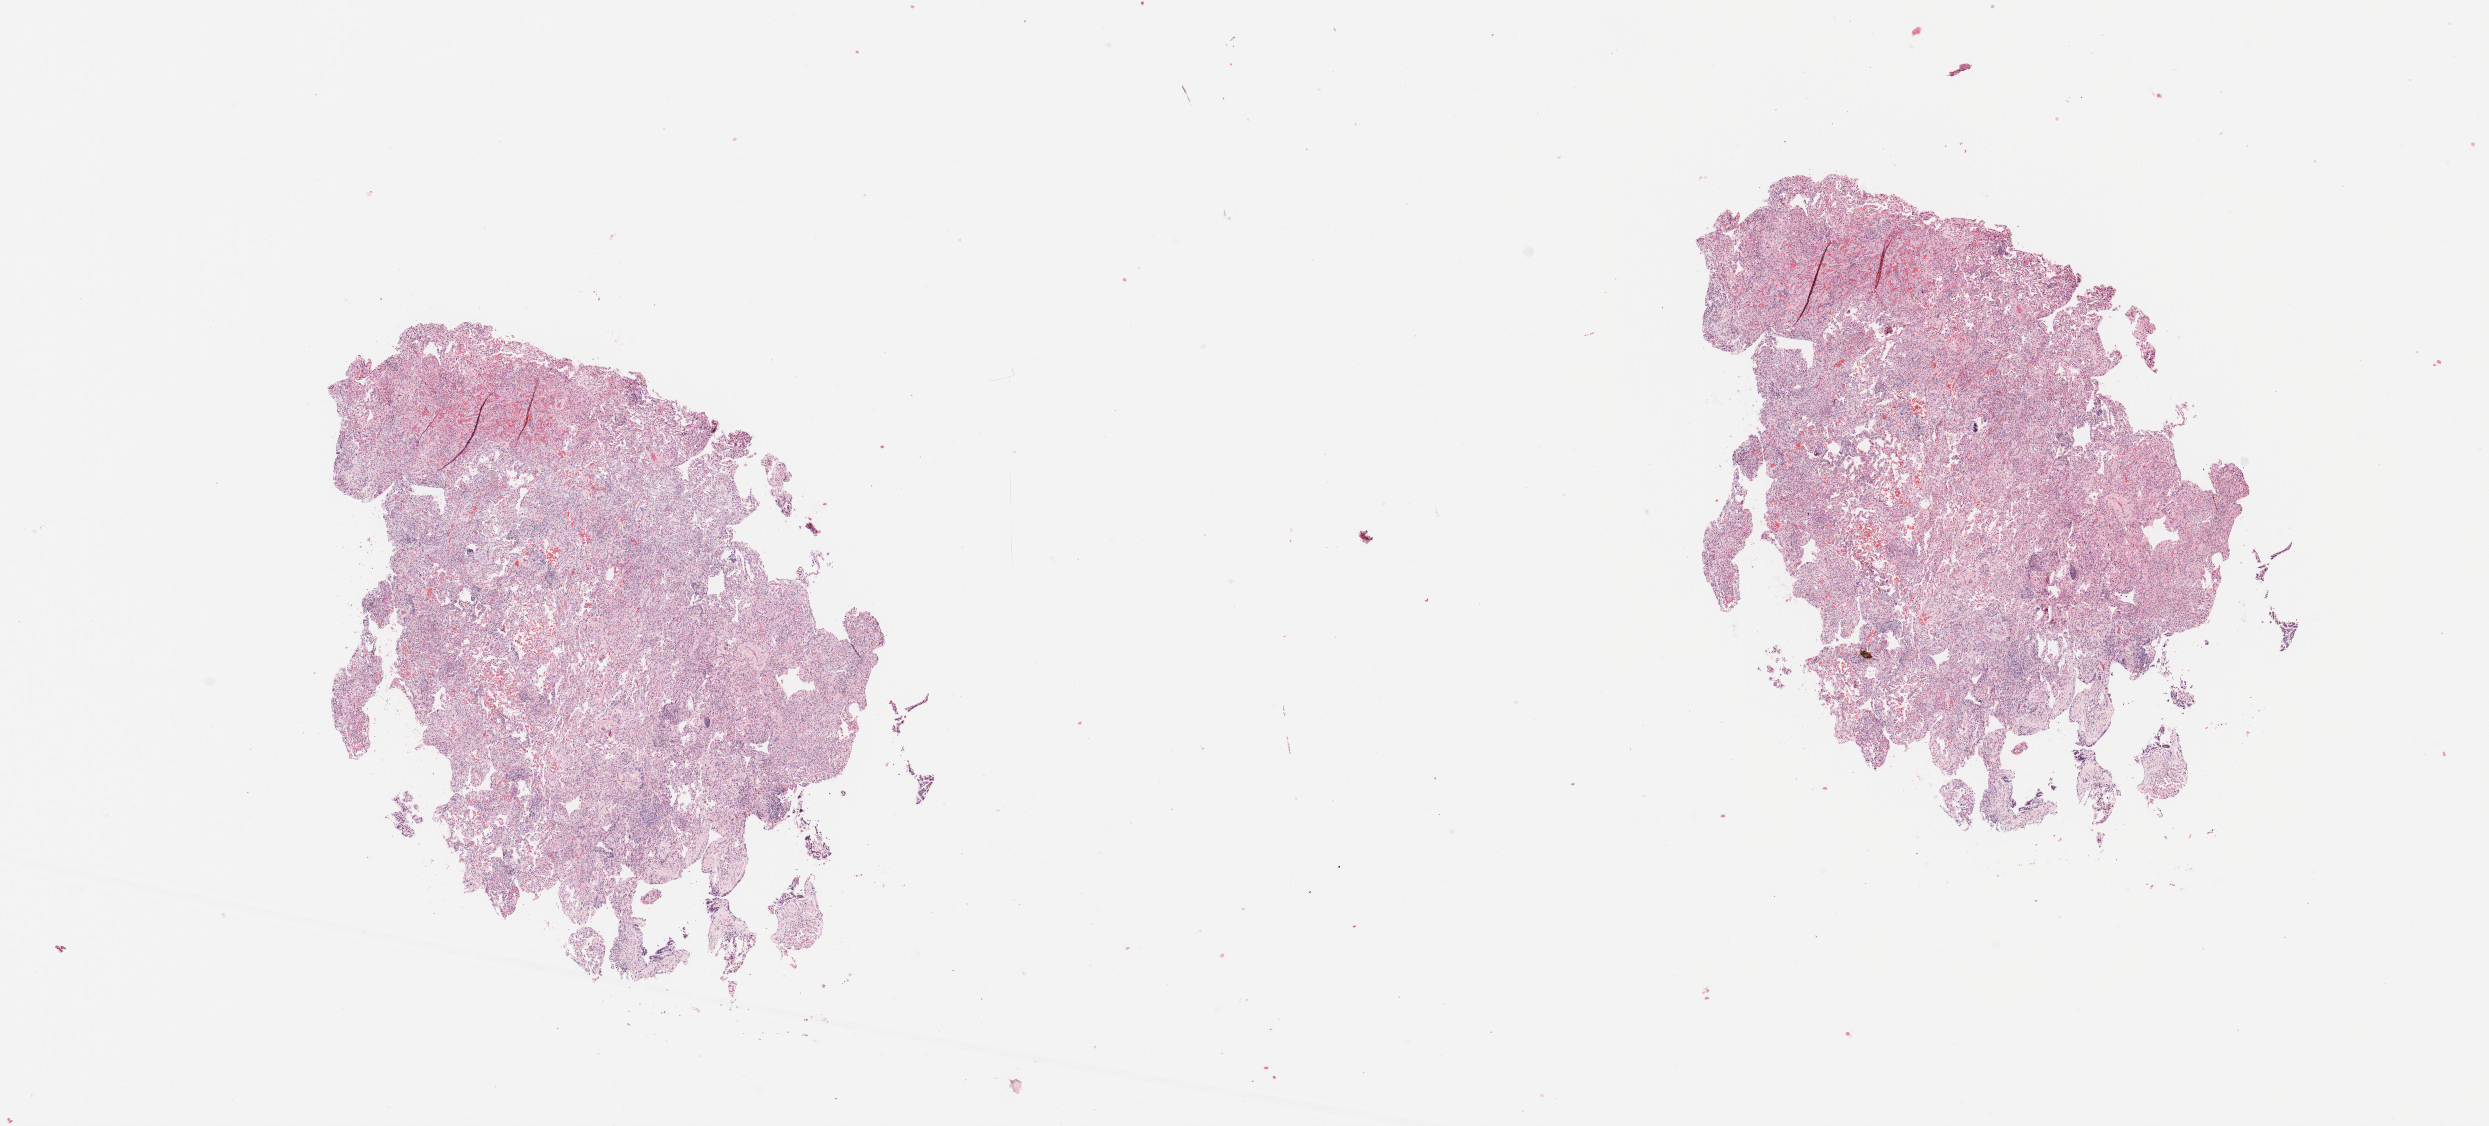
Digitized Hematoxylin and eosin (H&E) stained tissue section (whole slide) — a low-resolution overview of the entire scanned area, about 19.7 x 8.9 mm (from a 20x scan). Normal (non-tumour) tissue sample, sampled site: lung. 46-year-old male patient.
This section: normal (non-tumour) tissue from the same patient. Patient diagnosis: Adenocarcinoma, NOS.